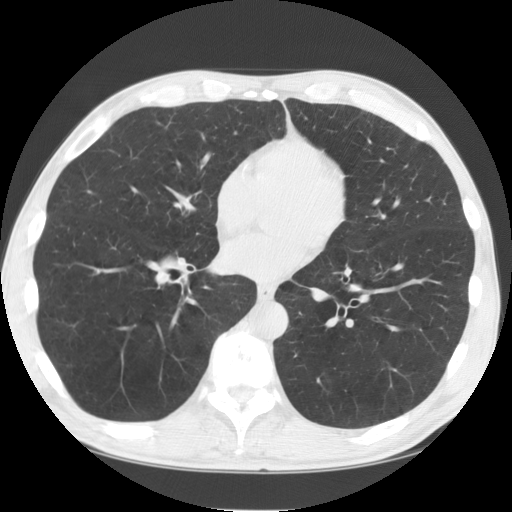
Chest CT (low-dose screening protocol), one axial image, baseline annual screen, lung window (W 1500 / L -600 HU), 2.5 mm slice thickness, standard (soft-tissue) reconstruction kernel (STANDARD), 120 kVp. Male participant, aged 60 years at enrolment.
• Expert reader's lesion annotation, bounding box <121,237,162,275> (left, top, right, bottom; pixels).
• No non-calcified nodule or mass ≥4 mm was recorded by the screening reader at this exam.
• Official screen result: negative screen, minor abnormalities not suspicious for lung cancer.